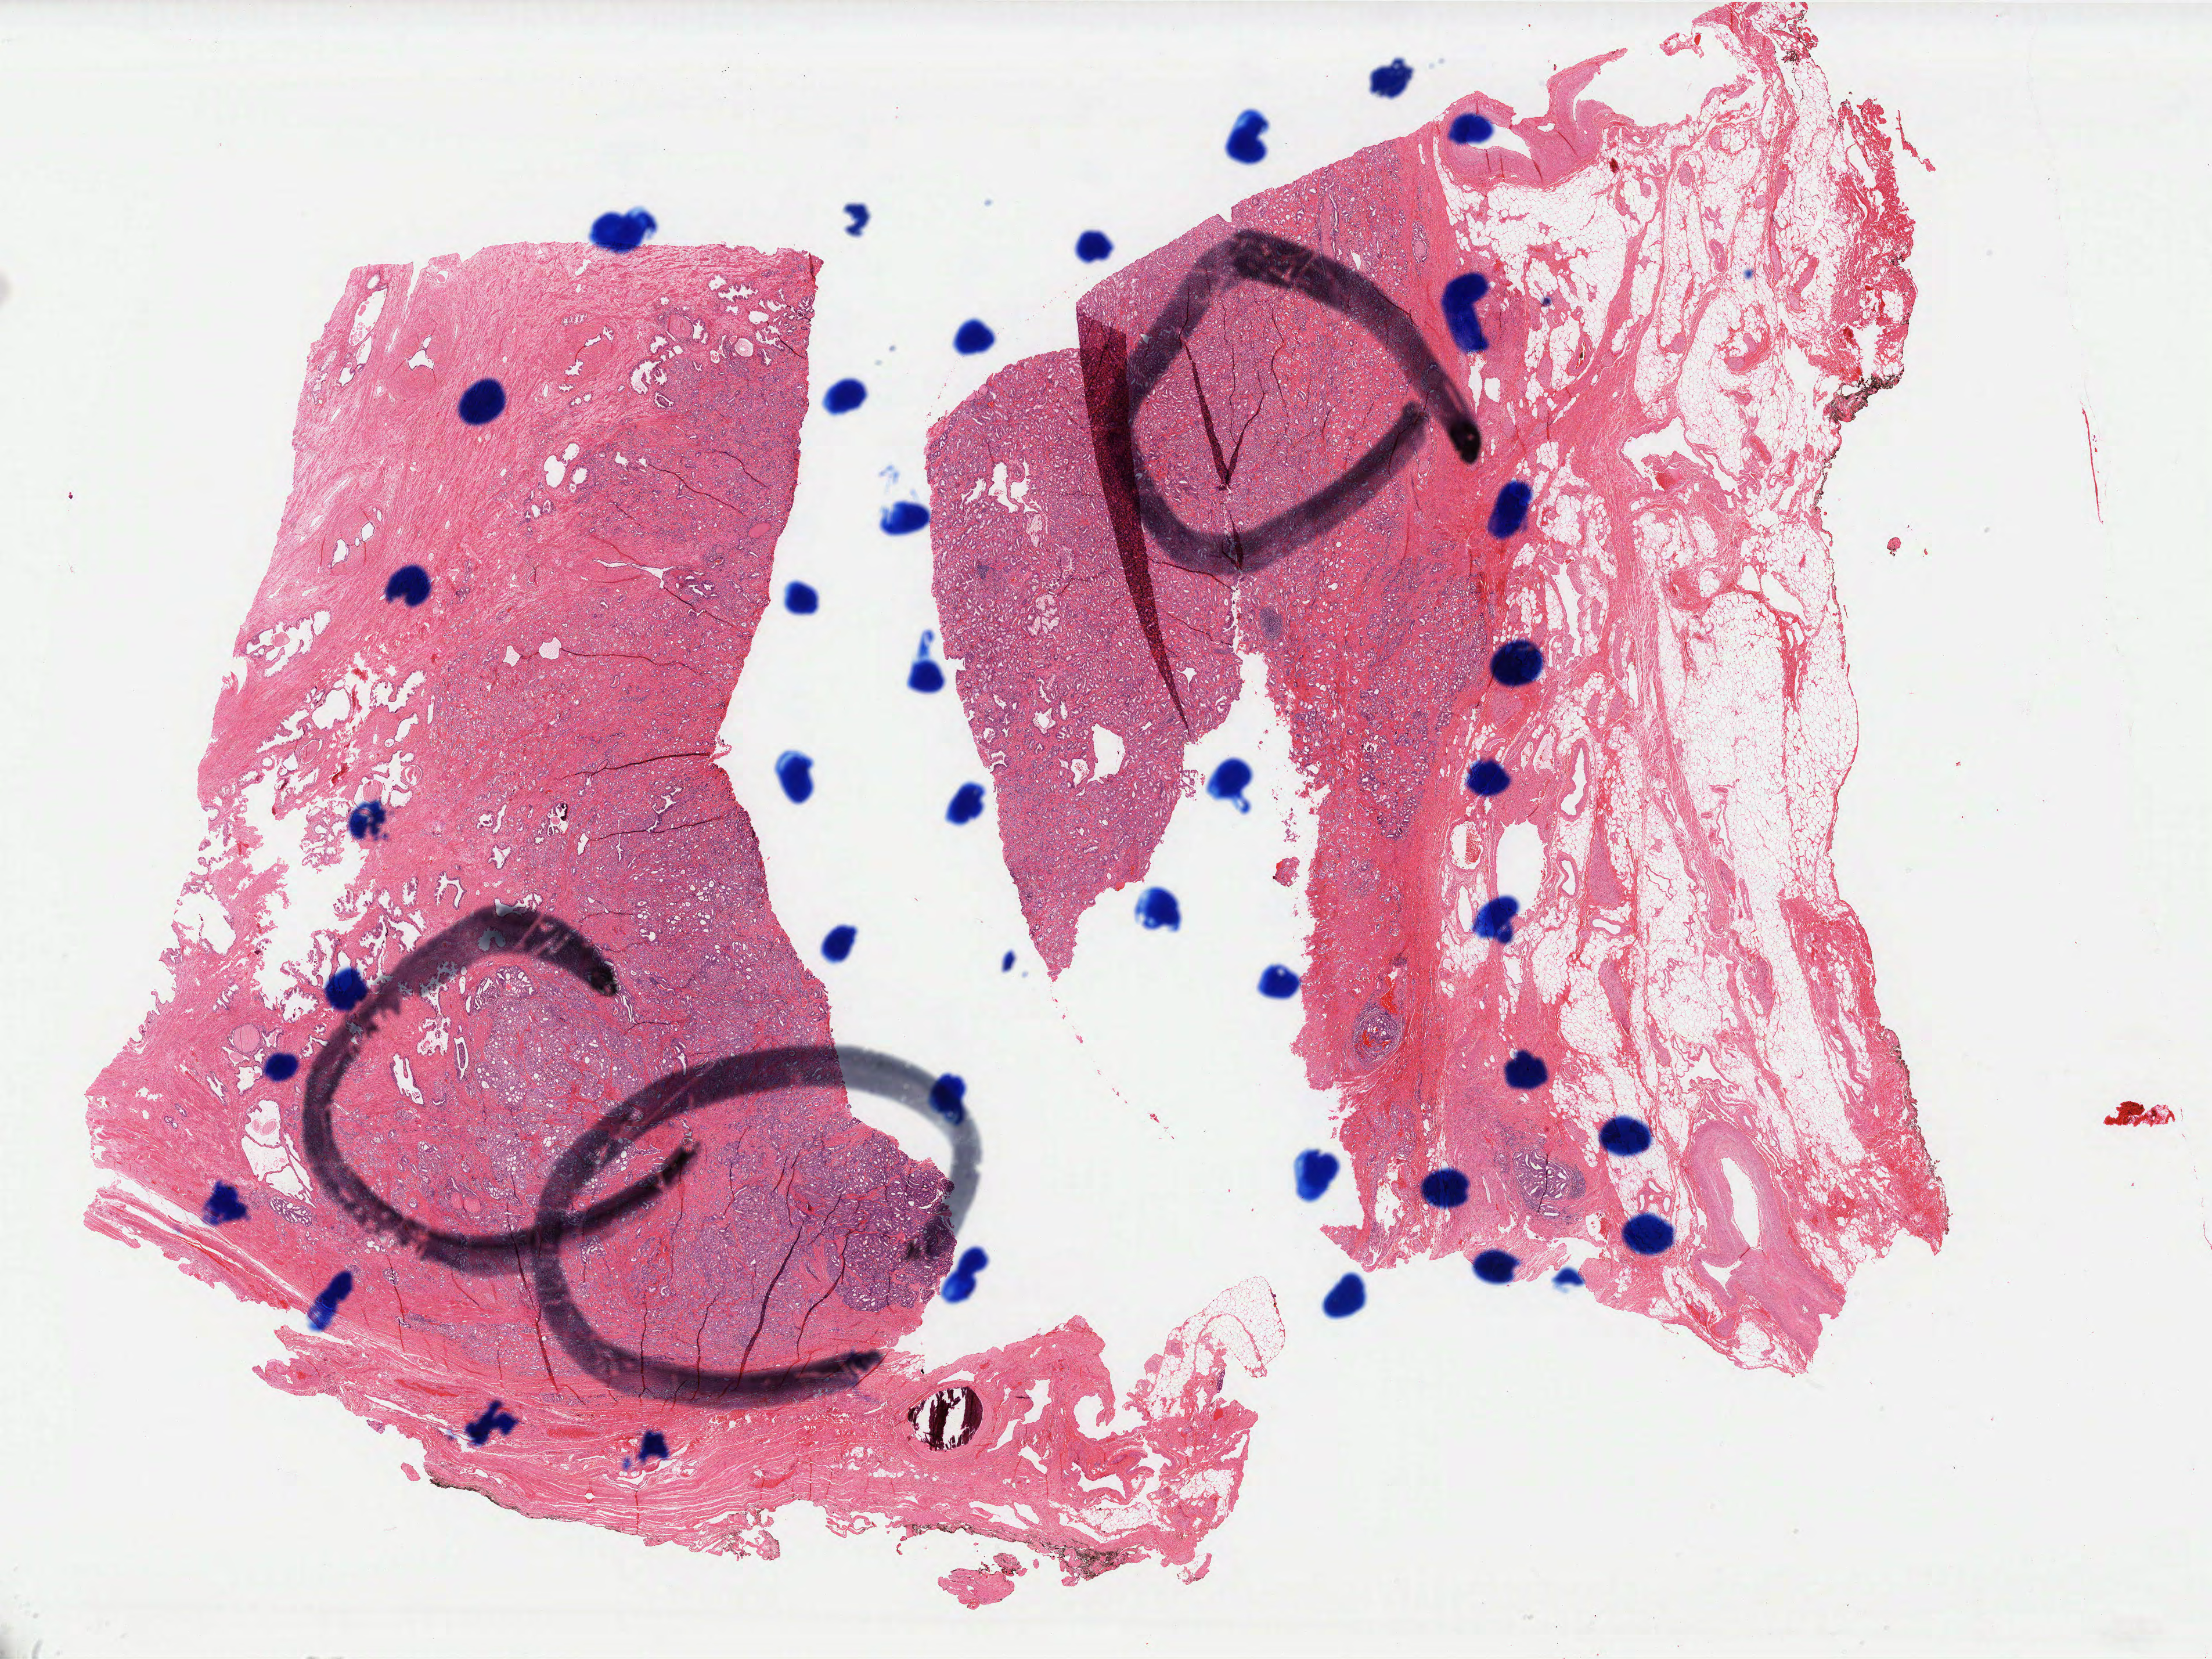
Whole-slide histology image, H&E-stained — a low-resolution overview of the entire scanned area, about 30.5 x 22.9 mm (acquisition: 40x scan). Formalin-fixed paraffin-embedded (FFPE) diagnostic section. Sample: primary tumour, prostate. Male patient; age at initial diagnosis 67 years. Gleason score: 7 (3+4).
• diagnosis: Adenocarcinoma, NOS (prostate gland)
• lymph nodes positive (case pathology): 0 of 4 examined
• laterality: bilateral